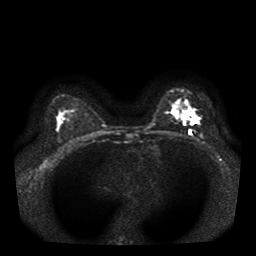
Breast MRI, one axial slice; position 27 of 41 along the scan axis; diffusion-weighted series; image 2 of 4 stored at this slice position (different b-values; order by instance number); 1.5 T; 5 mm slice thickness; 256 × 256 image matrix, field of view 330 × 330 mm. Female patient.
Structures marked on this image (outlined manually by an expert reader):
- tumour on diffusion-weighted imaging: bounding box <179,113,196,125> (left, top, right, bottom; pixels)